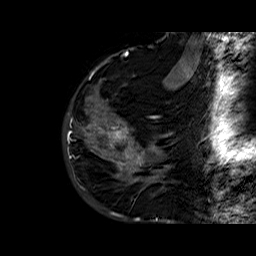
Breast MRI (dynamic contrast-enhanced), one sagittal slice. Slice 15 of 60 in the series (ordered by position). Dynamic contrast-enhanced series, time point 2 of 6 at this slice position (early post-contrast). 1.5 T. TE 6.4 ms, TR 32.8 ms. 4 mm slice thickness. 256 × 256 image matrix, field of view 200 × 200 mm. Female patient. Case-level facts recorded for this patient, not image findings: setting: breast cancer imaged before/during neoadjuvant chemotherapy; receptor status: HR-positive, HER2-negative.
Annotated regions visible in this slice (semi-automatic segmentation, software-assisted and operator-edited):
- analysis volume of interest (the breast-tissue region the enhancement analysis was run in; not a lesion): bounding box <86,77,163,177> (left, top, right, bottom; pixels)
- tumour enhancement mask (voxels above the 100 % enhancement threshold inside the analysis volume of interest): <110,126,144,165>